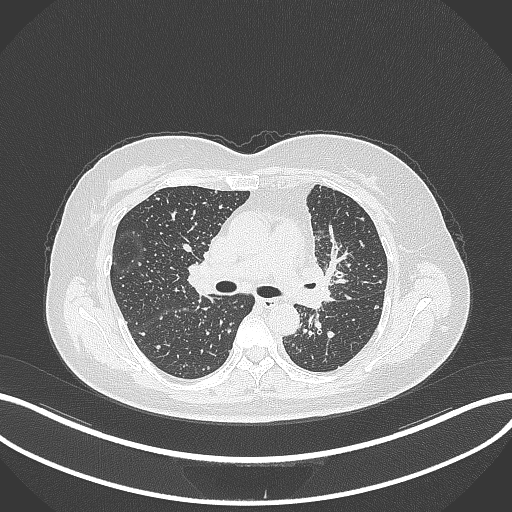
Chest CT, one axial slice; position 204 of 348 along the scan axis; 120 kVp; lung window (W 1500 / L -600 HU); 512 × 512 image matrix, field of view 400 × 400 mm. Female patient, age 49 years. Case-level facts recorded for this patient, not image findings: clinical TNM (as recorded): T1c N0 M1.
Structures marked on this image (rectangle marked by the reading radiologist):
- lung tumour (recorded histology: adenocarcinoma): box from (x=298, y=253) to (x=333, y=311) px